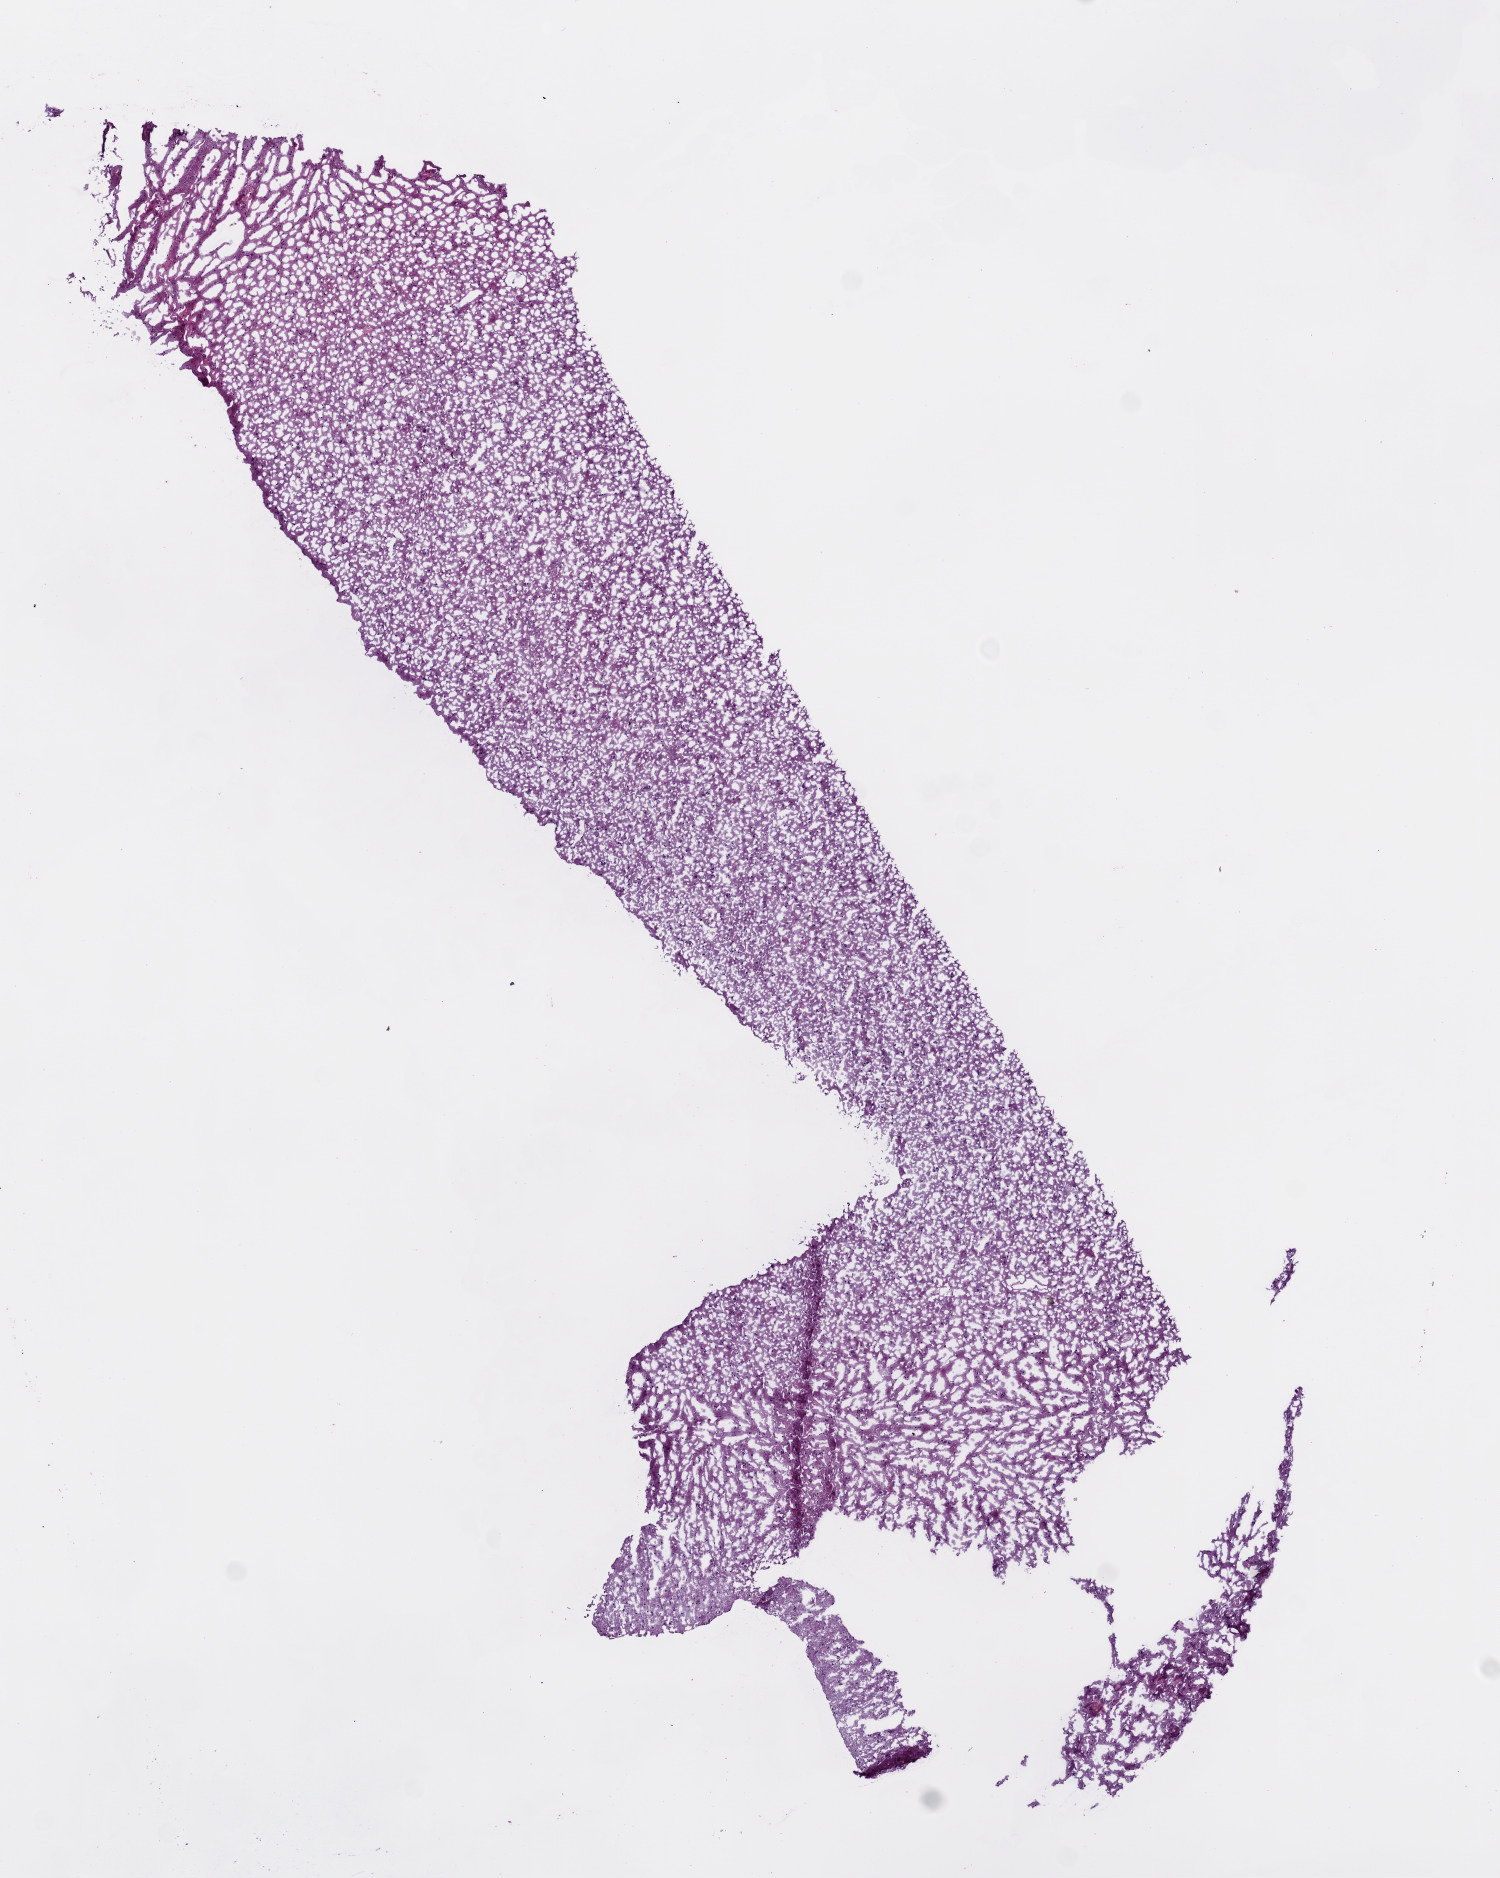
Hematoxylin and eosin (H&E) stained whole-slide image — low-resolution overview of the scanned area, about 6.0 x 7.5 mm (acquisition: 20x scan); frozen section; brain, primary tumour sample. Female patient; age at initial diagnosis 38 years. Histologic grade: G3 (poorly differentiated). Composition of this section per pathologist review: tumour cells 100%, tumour nuclei 60%, normal cells 0%, stromal cells 0%, necrosis 0%.
Histologic diagnosis: Mixed glioma (cerebrum).